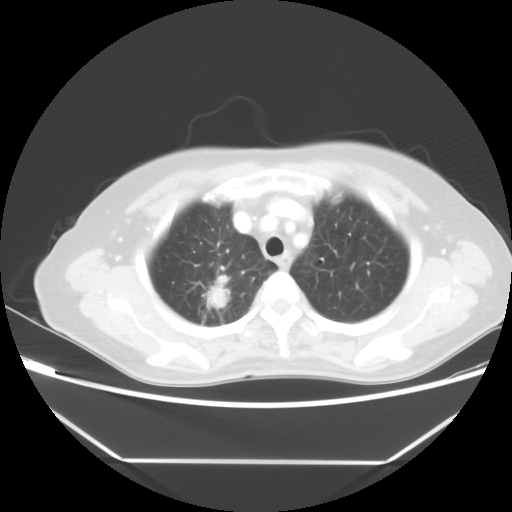
Chest CT, one axial slice. Lung window (W 1500 / L -600 HU). 5 mm slice thickness. 512 × 512 image matrix. Female patient, age 65 years. From the clinical record (not read from this slice): clinical TNM (as recorded): T1c N1 M1.
Structures marked on this image (rectangle marked by the reading radiologist):
- lung tumour (recorded histology: adenocarcinoma): bounding box <202,268,239,319> (left, top, right, bottom; pixels)